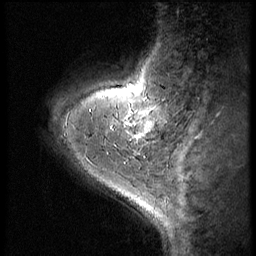
Breast MRI (dynamic contrast-enhanced), one sagittal slice. Position 13 of 56 along the scan axis. Dynamic contrast-enhanced series, image 2 of 3 at this slice position (ordered by acquisition). 1.5 T. TE 4.2 ms, TR 9 ms. 2.5 mm slice thickness. 256 × 256 image matrix, field of view 180 × 180 mm. Patient: female, 38 years. From the clinical record (not read from this slice): setting: breast cancer imaged before/during neoadjuvant chemotherapy; receptor status: triple-negative.
Structures marked on this image (semi-automatic segmentation, software-assisted and operator-edited):
- analysis volume of interest (the breast-tissue region the enhancement analysis was run in; not a lesion): bounding box <107,95,179,149> (left, top, right, bottom; pixels)
- tumour enhancement mask (voxels above the 140 % enhancement threshold inside the analysis volume of interest): <129,123,151,137>